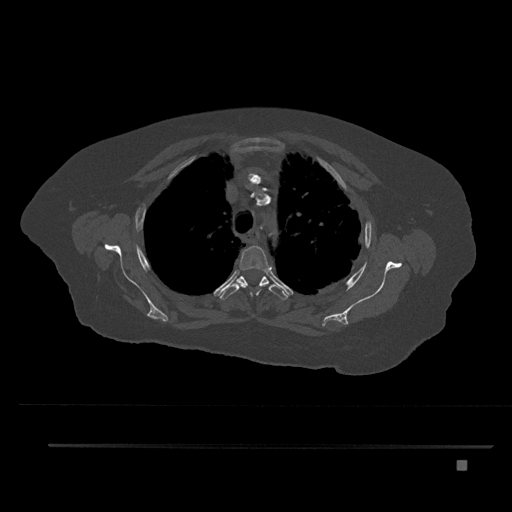
CT including the spine, one axial slice. Position 620 of 797 along the scan axis. Reconstruction kernel Br40s/3. 120 kVp. Bone window (W 1800 / L 400 HU). 0.5 mm slice thickness. 512 × 512 image matrix, field of view 437 × 437 mm. Female patient, age 76 years. Case-level facts recorded for this patient, not image findings: primary cancer: lung.
Outlined on this slice (semi-automatic segmentation, software-assisted and operator-edited):
- T3 vertebra: bounding box (x1, y1, x2, y2) in pixels: (232, 245, 271, 296)
- T4 vertebra: (219, 276, 288, 300)